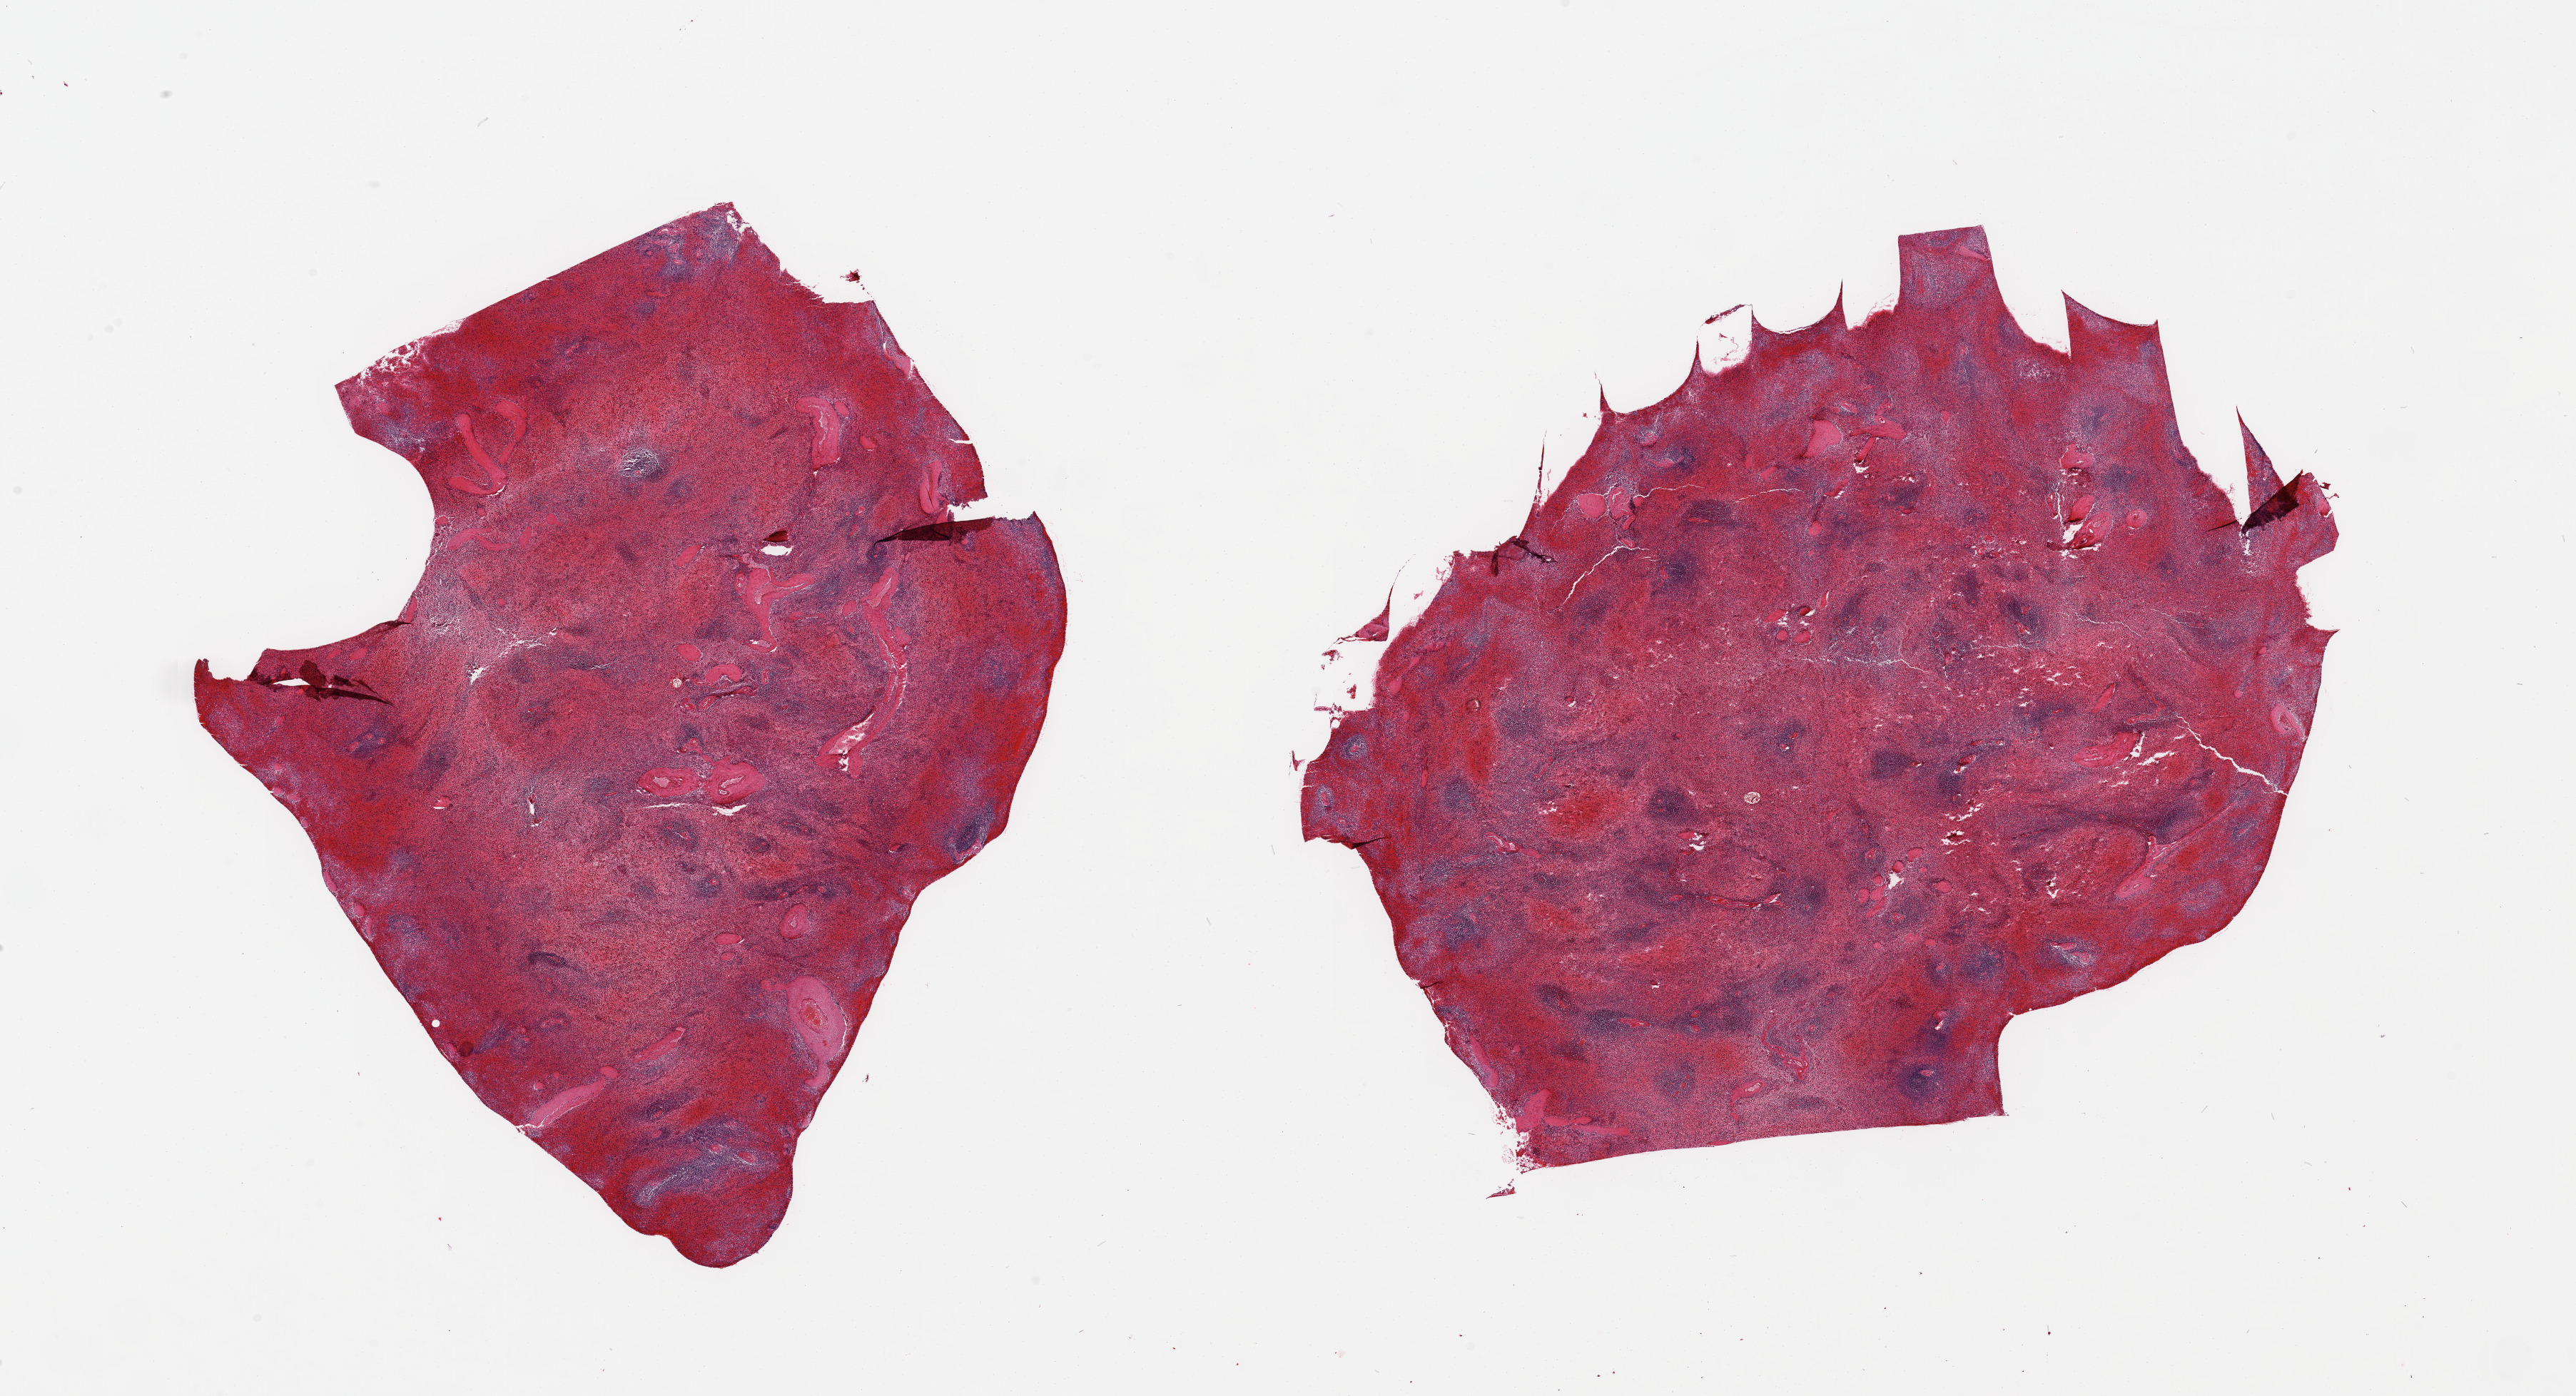
H&E whole-slide image — a low-resolution overview of the entire scanned area, about 28.5 x 15.5 mm (acquisition: 20x scan). PAXgene-fixed paraffin-embedded (PFPE) section. Target tissue: spleen. Donor tissue sample. Donor sex: male.
Pathologist's review note for this sample: 2 pieces; moderate to severe red pulp vascular congestion.